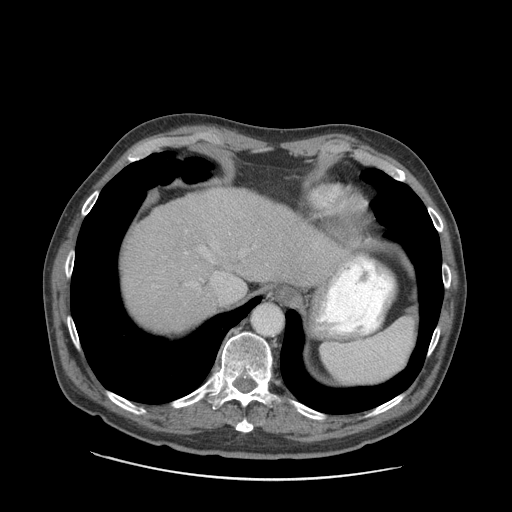
Contrast-enhanced abdominal CT (liver protocol), one axial slice. Slice 74 of 89 in the series (ordered by position). Reconstruction kernel STANDARD. Soft-tissue window (W 400 / L 40 HU). 2.5 mm slice thickness. 512 × 512 image matrix, field of view 420 × 420 mm. Case-level facts recorded for this patient, not image findings: diagnosis: hepatocellular carcinoma (patient treated with transarterial chemoembolisation; whether this scan precedes or follows treatment is not stated here); TNM stage (as recorded): Stage-I; Child-Pugh class: A; tumour differentiation: moderately differentiated; tumour size: 4.6 cm.
Structures marked on this image (semi-automatic segmentation, software-assisted and operator-edited):
- liver parenchyma outside the tumour (the mass and vessels are separate outlines, so this box may not span the whole liver): bounding box [x1, y1, x2, y2] px = [122, 188, 350, 332]
- liver vessels: [185, 246, 244, 298]